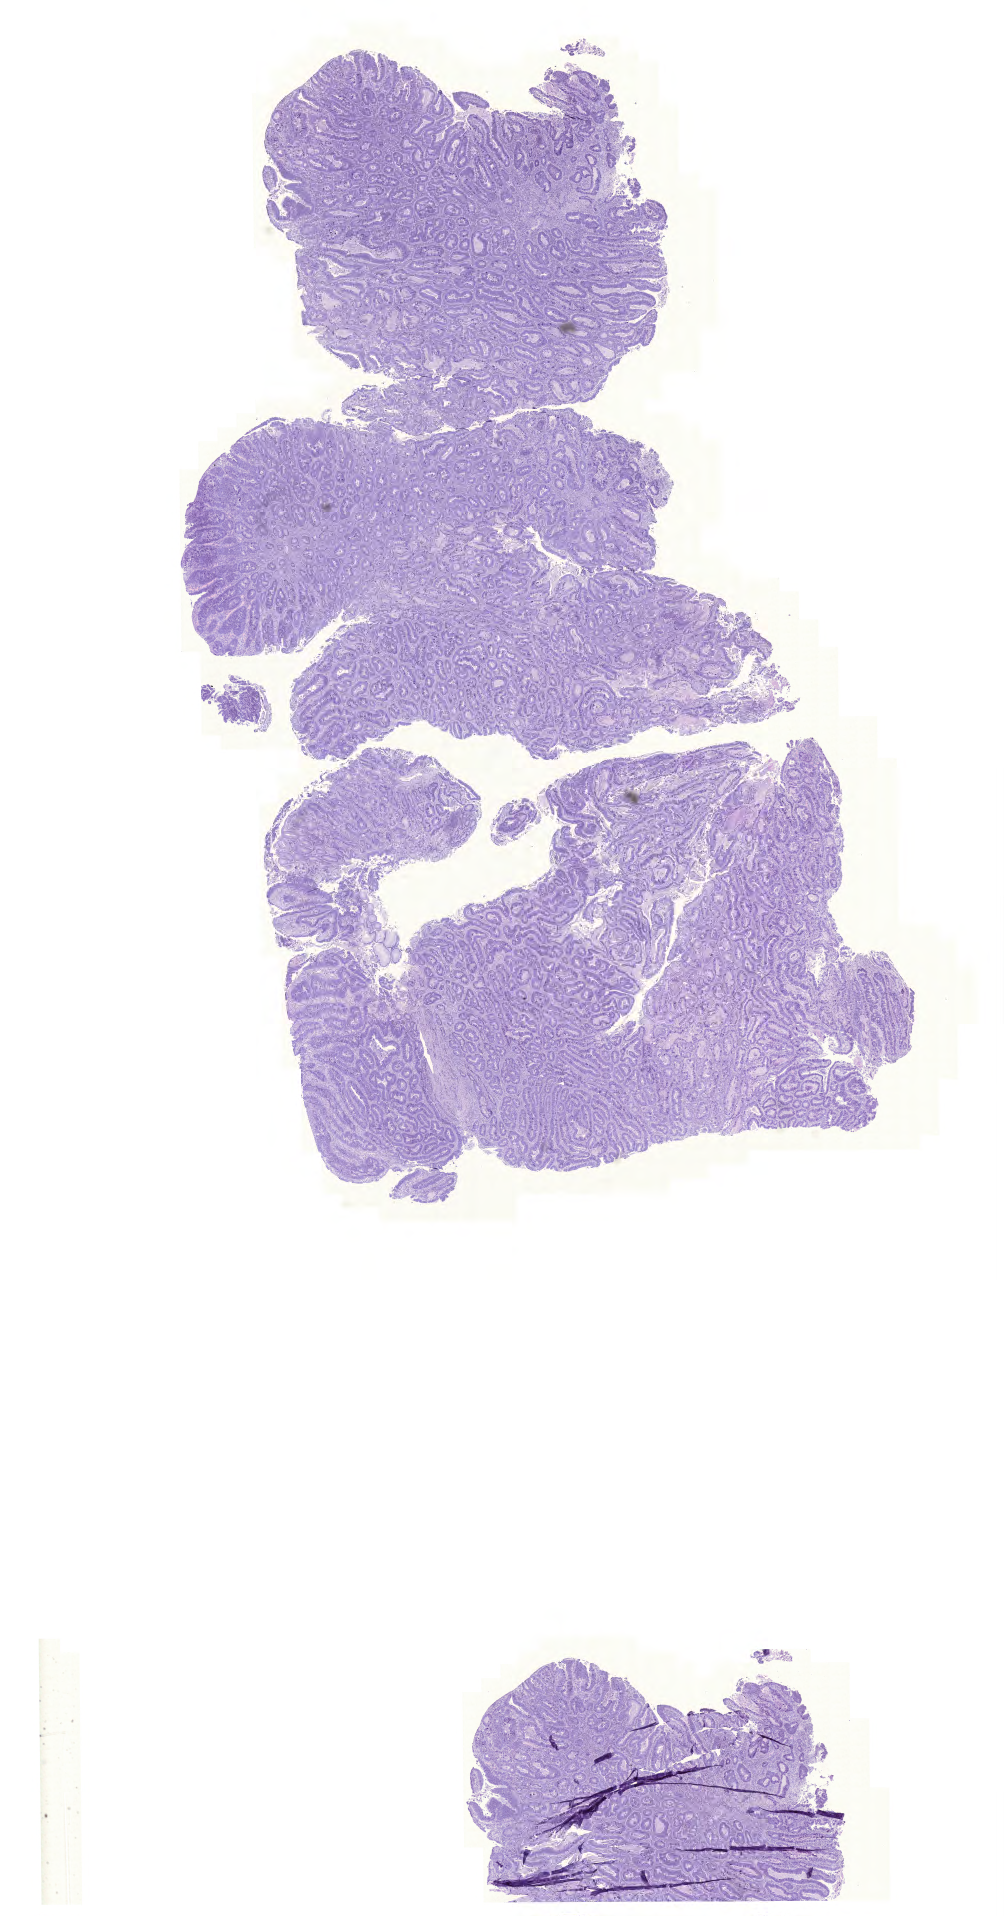
Whole-slide histology image, H&E — low-resolution overview of the scanned area, about 14.9 x 28.5 mm; formalin-fixed paraffin-embedded (FFPE) diagnostic section; rectum, primary tumour sample. Patient: female, age at initial diagnosis 72 years.
Lymph nodes positive (case pathology): 0 of 38 examined. Pathologic diagnosis: Adenocarcinoma, NOS (rectosigmoid junction). AJCC pathologic stage: IIA.